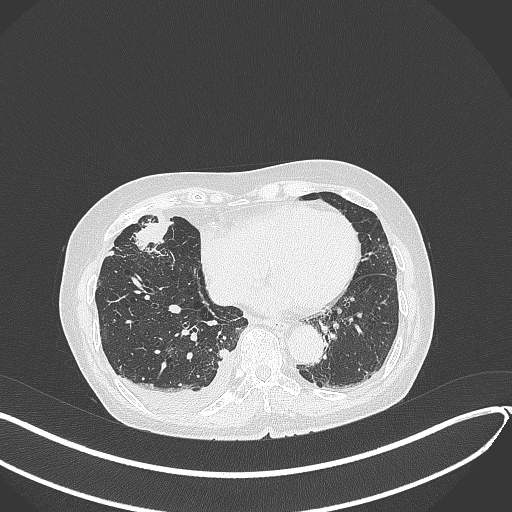
Chest CT, one axial slice; slice 127 of 418 in the series (ordered by position); 120 kVp; lung window (W 1500 / L -600 HU); 512 × 512 image matrix, field of view 400 × 400 mm. Female patient, age 75 years. From the clinical record (not read from this slice): clinical TNM (as recorded): T2a N3 M0.
Structures marked on this image (rectangle marked by the reading radiologist):
- lung tumour (recorded histology: adenocarcinoma): bounding box [x1, y1, x2, y2] px = [134, 215, 173, 251]